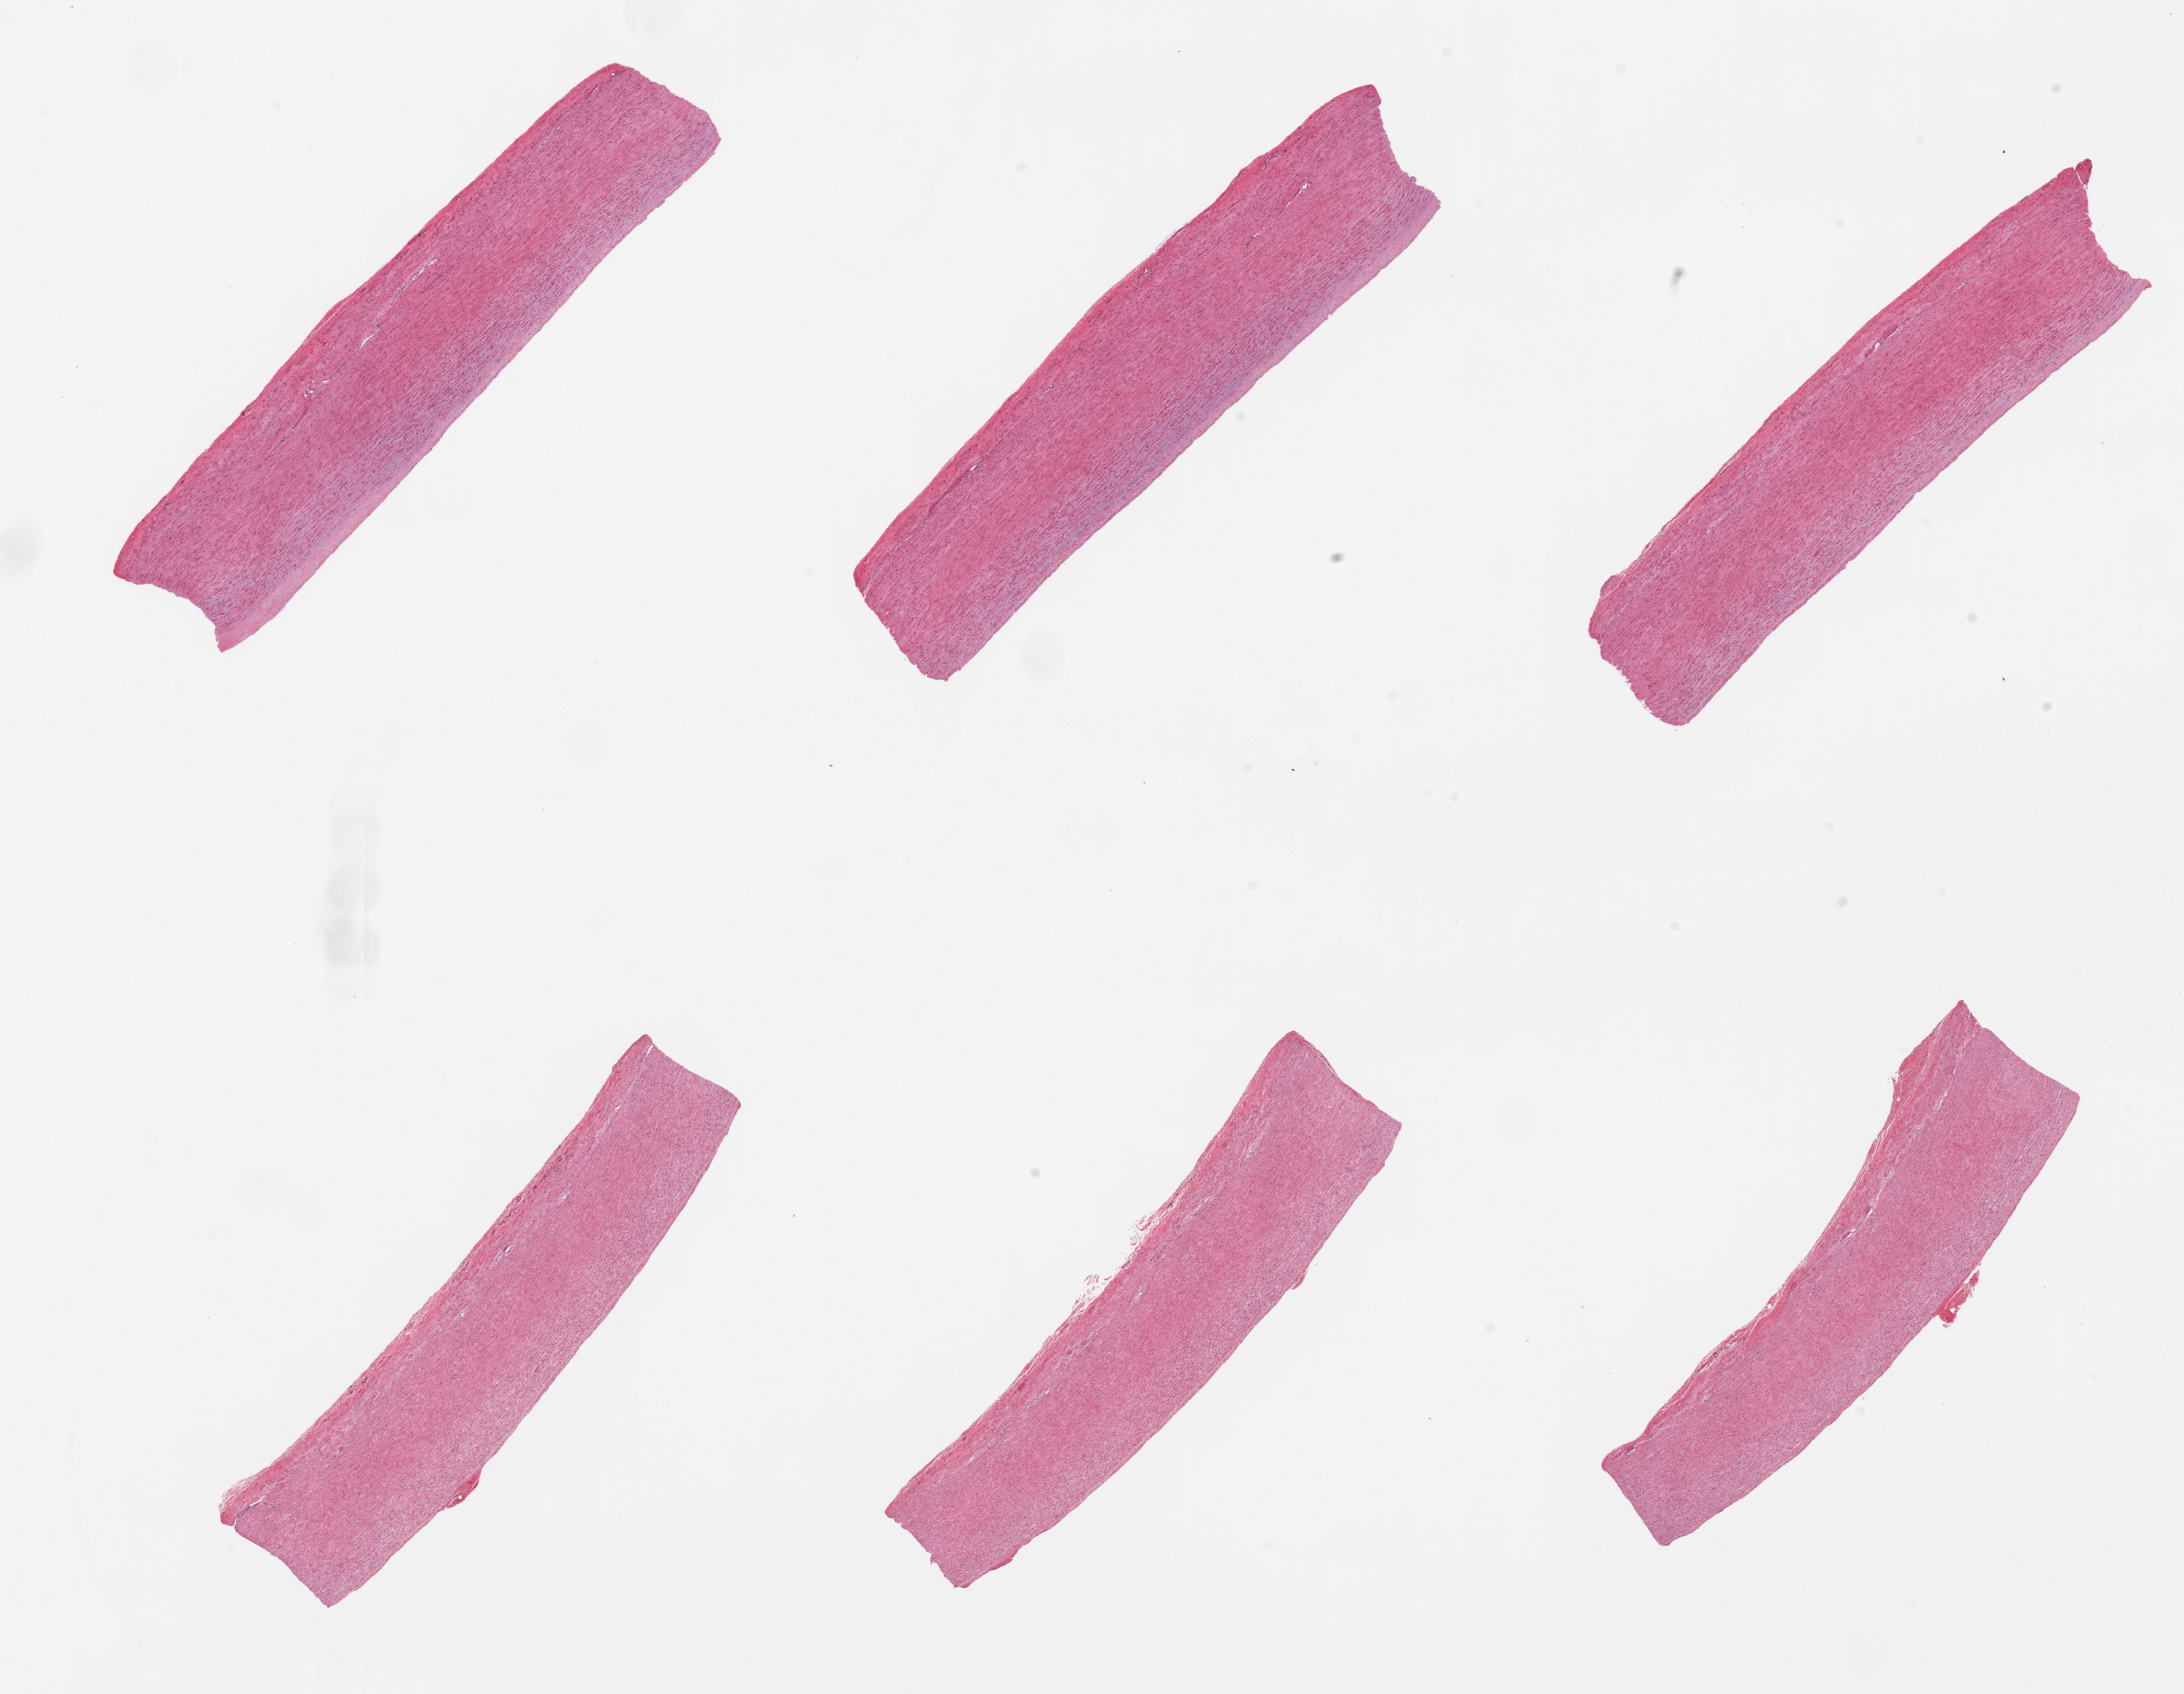
H&E whole-slide image, brightfield, low-resolution overview of the scanned area, about 23.6 x 18.3 mm (slide scanned at 20x), PAXgene-fixed paraffin-embedded (PFPE) section, sampled site (target tissue): aorta, donor tissue sample.
Review note (as recorded): 6 pieces, well trimmed, focal mild atherosclerosis.